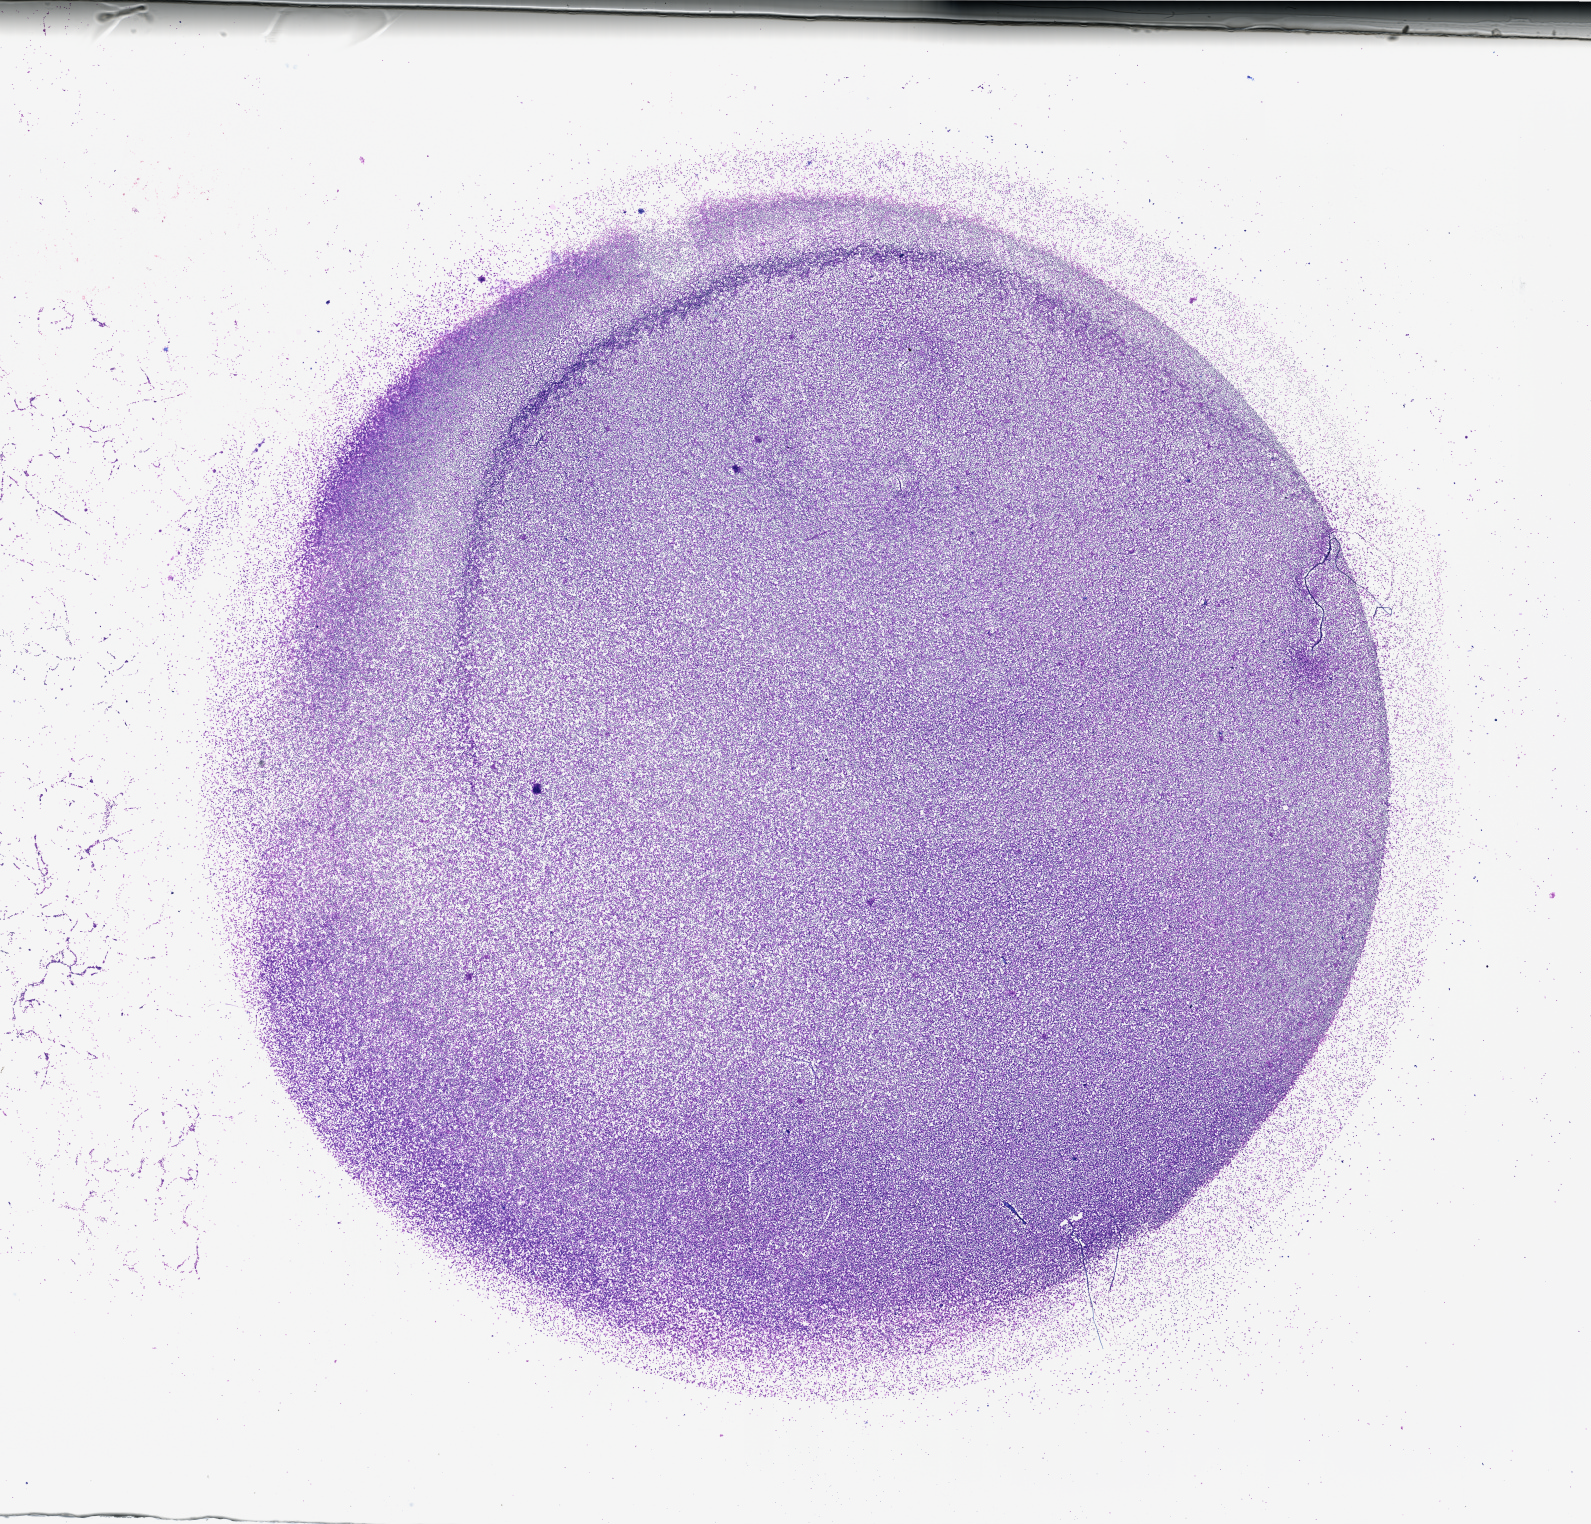
Digitized H&E tissue section (whole slide), shown as a low-resolution overview of the whole scanned area (about 25.1 x 24.1 mm). Bone marrow (leukaemic) sample. 75-year-old female patient. Blasts: 80%.
Diagnosis: Acute Myeloid Leukemia. WHO classification: AML with maturation. FAB classification: M2.